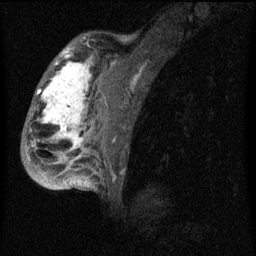
Breast MRI (dynamic contrast-enhanced), one sagittal slice. Position 43 of 60 along the scan axis. Dynamic contrast-enhanced series, image 2 of 4 at this slice position (ordered by acquisition). 1.5 T. TE 4.2 ms, TR 8 ms. 256 × 256 image matrix, field of view 180 × 180 mm. Female patient, age 50 years.
Structures marked on this image (semi-automatically segmented with operator editing):
- analysis volume of interest (the breast-tissue region the enhancement analysis was run in; not a lesion): bounding box (x1, y1, x2, y2) in pixels: (26, 44, 124, 177)
- tumour enhancement mask (voxels above the 70 % enhancement threshold inside the analysis volume of interest): (32, 48, 92, 177)